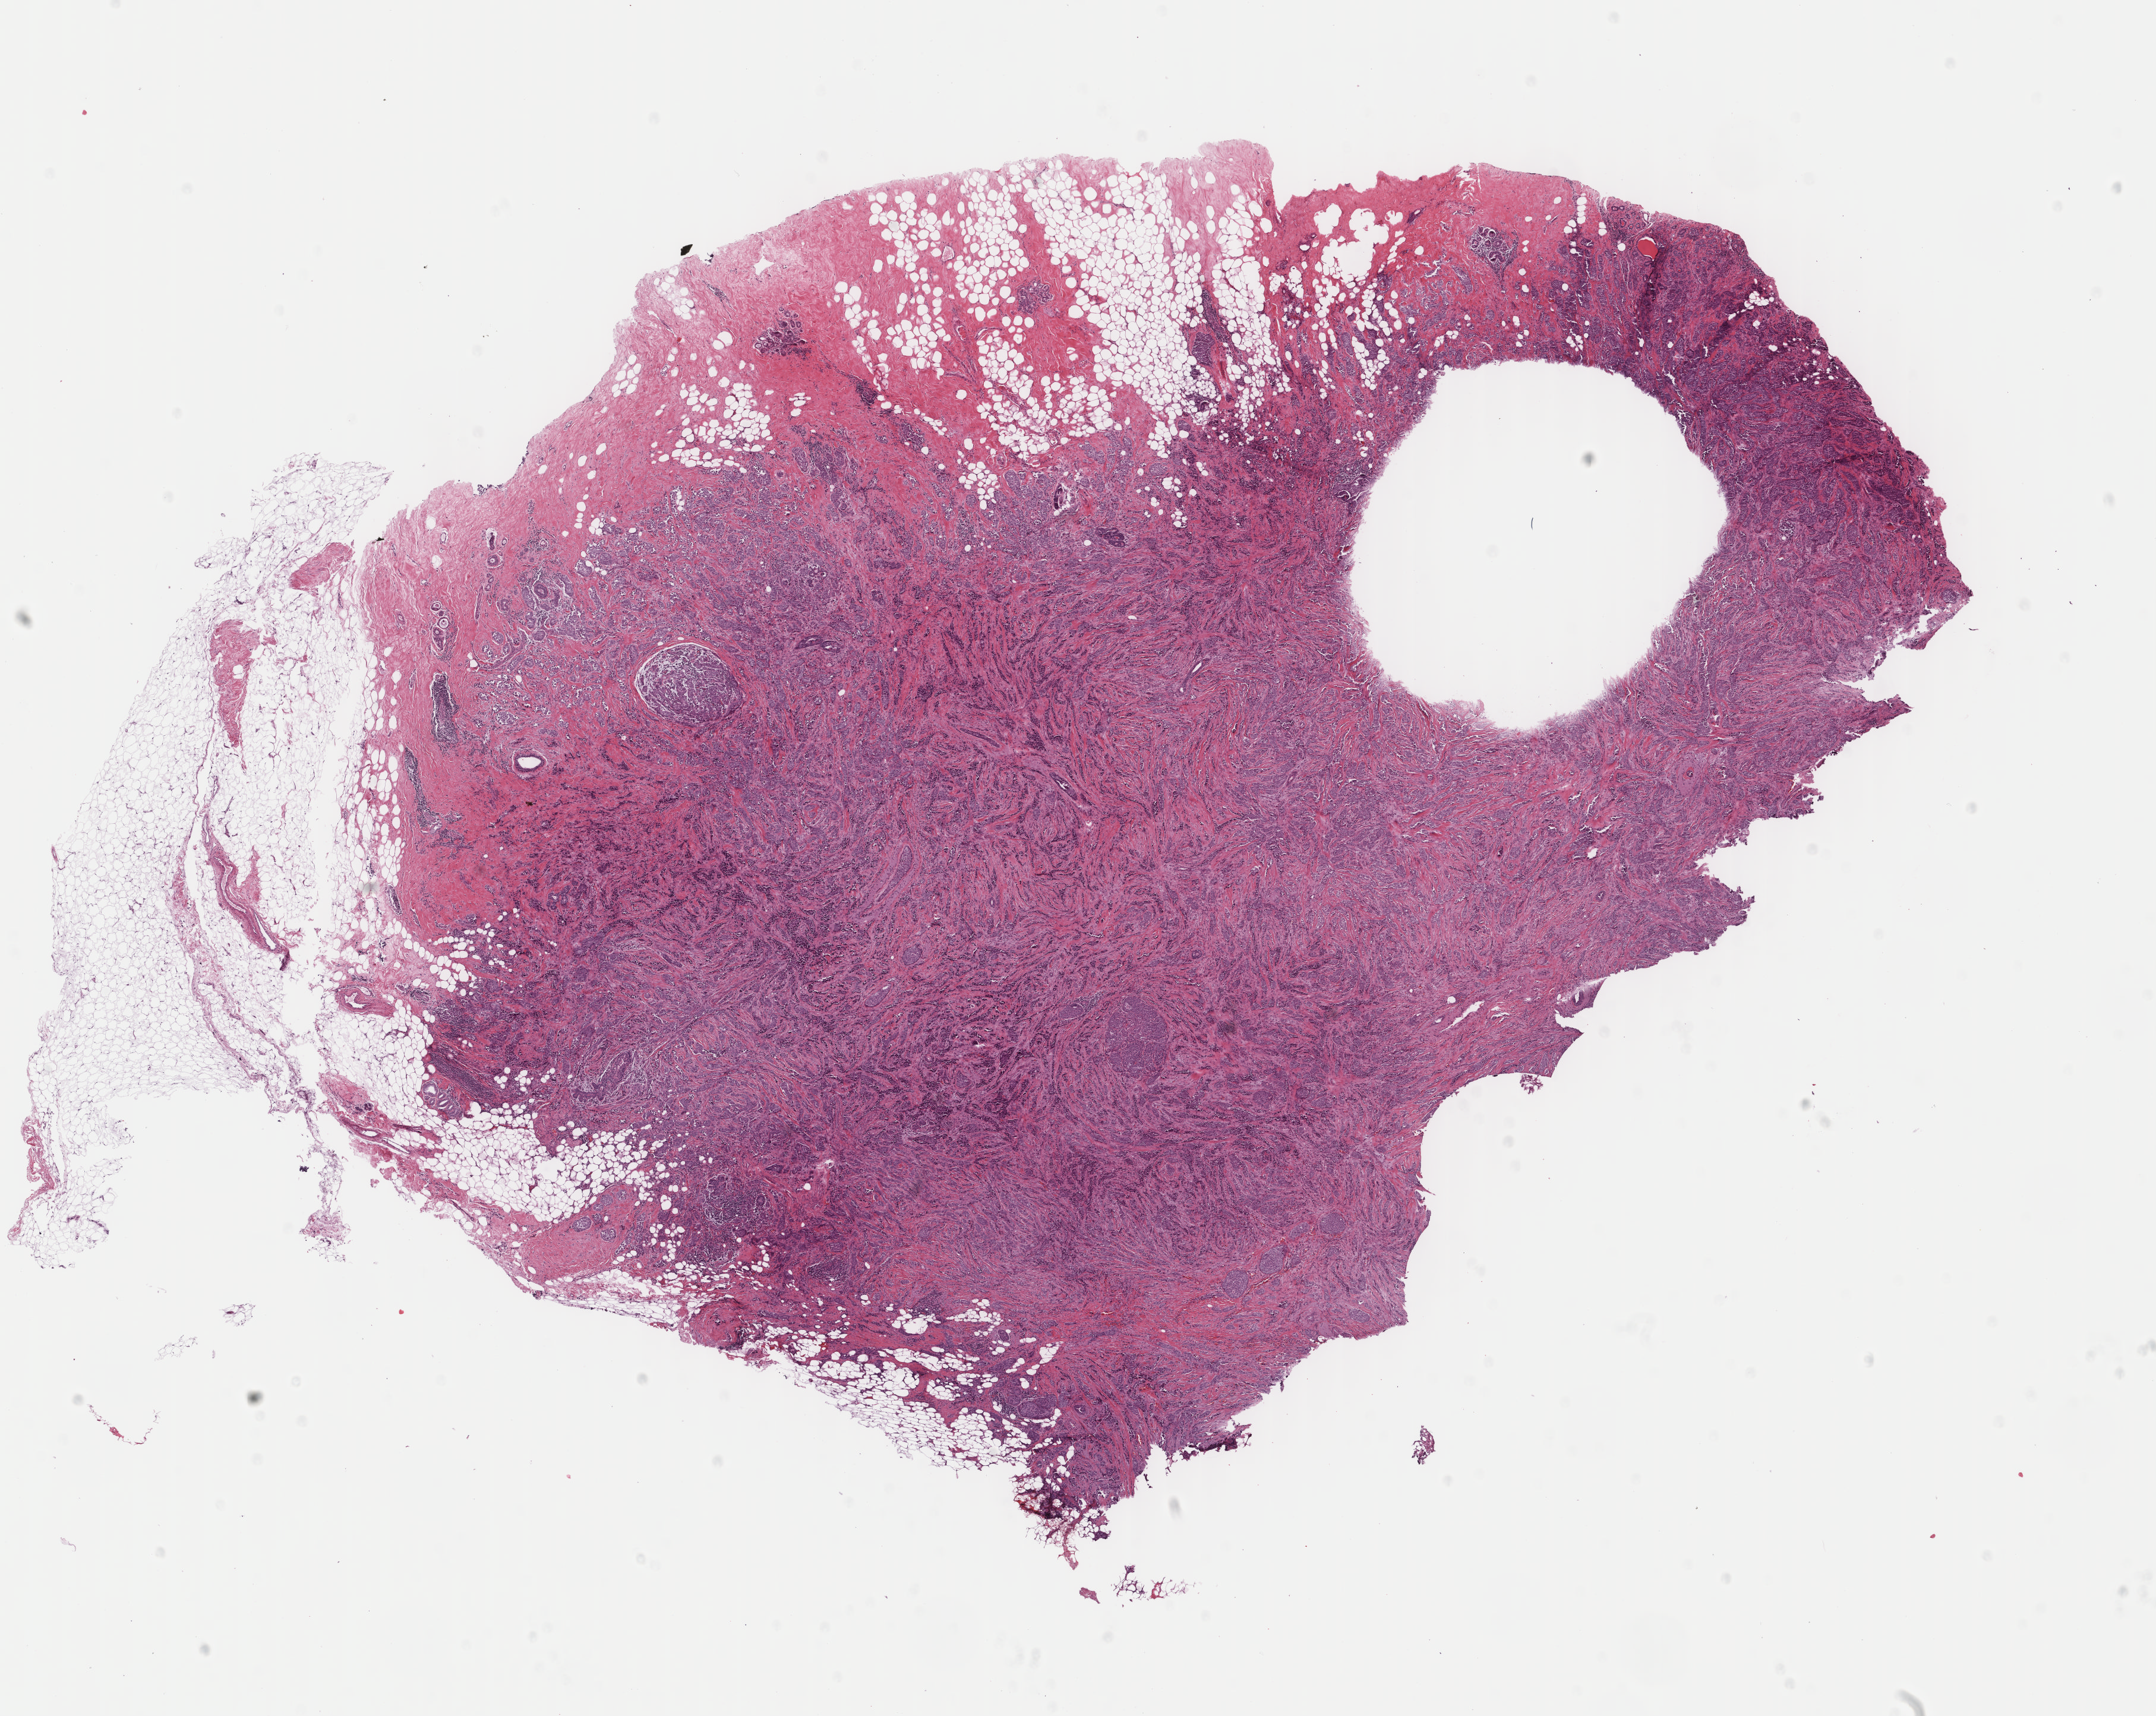
Whole-slide histology image, Hematoxylin and eosin (H&E) stained, whole scanned area (about 14.4 x 11.5 mm, from a 40x scan) shown as a low-resolution overview. Formalin-fixed paraffin-embedded (FFPE) diagnostic section. Primary tumour sample from the breast. Female patient; age at initial diagnosis 52 years.
AJCC pathologic stage: IIA (6th edition). Diagnosis: Infiltrating duct and lobular carcinoma.